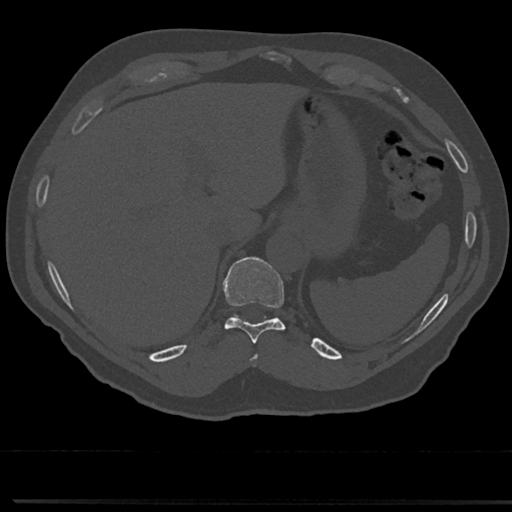
CT including the spine, one axial slice; position 250 of 817 along the scan axis; bone window (W 1800 / L 400 HU); 0.5 mm slice thickness; 512 × 512 image matrix. Patient: male, 61 years. Case-level facts recorded for this patient, not image findings: primary cancer: prostate.
Structures marked on this image (semi-automatic segmentation, software-assisted and operator-edited):
- T10 vertebra: box from (x=214, y=258) to (x=294, y=343) px
- T9 vertebra: (x=250, y=351)–(x=259, y=368)